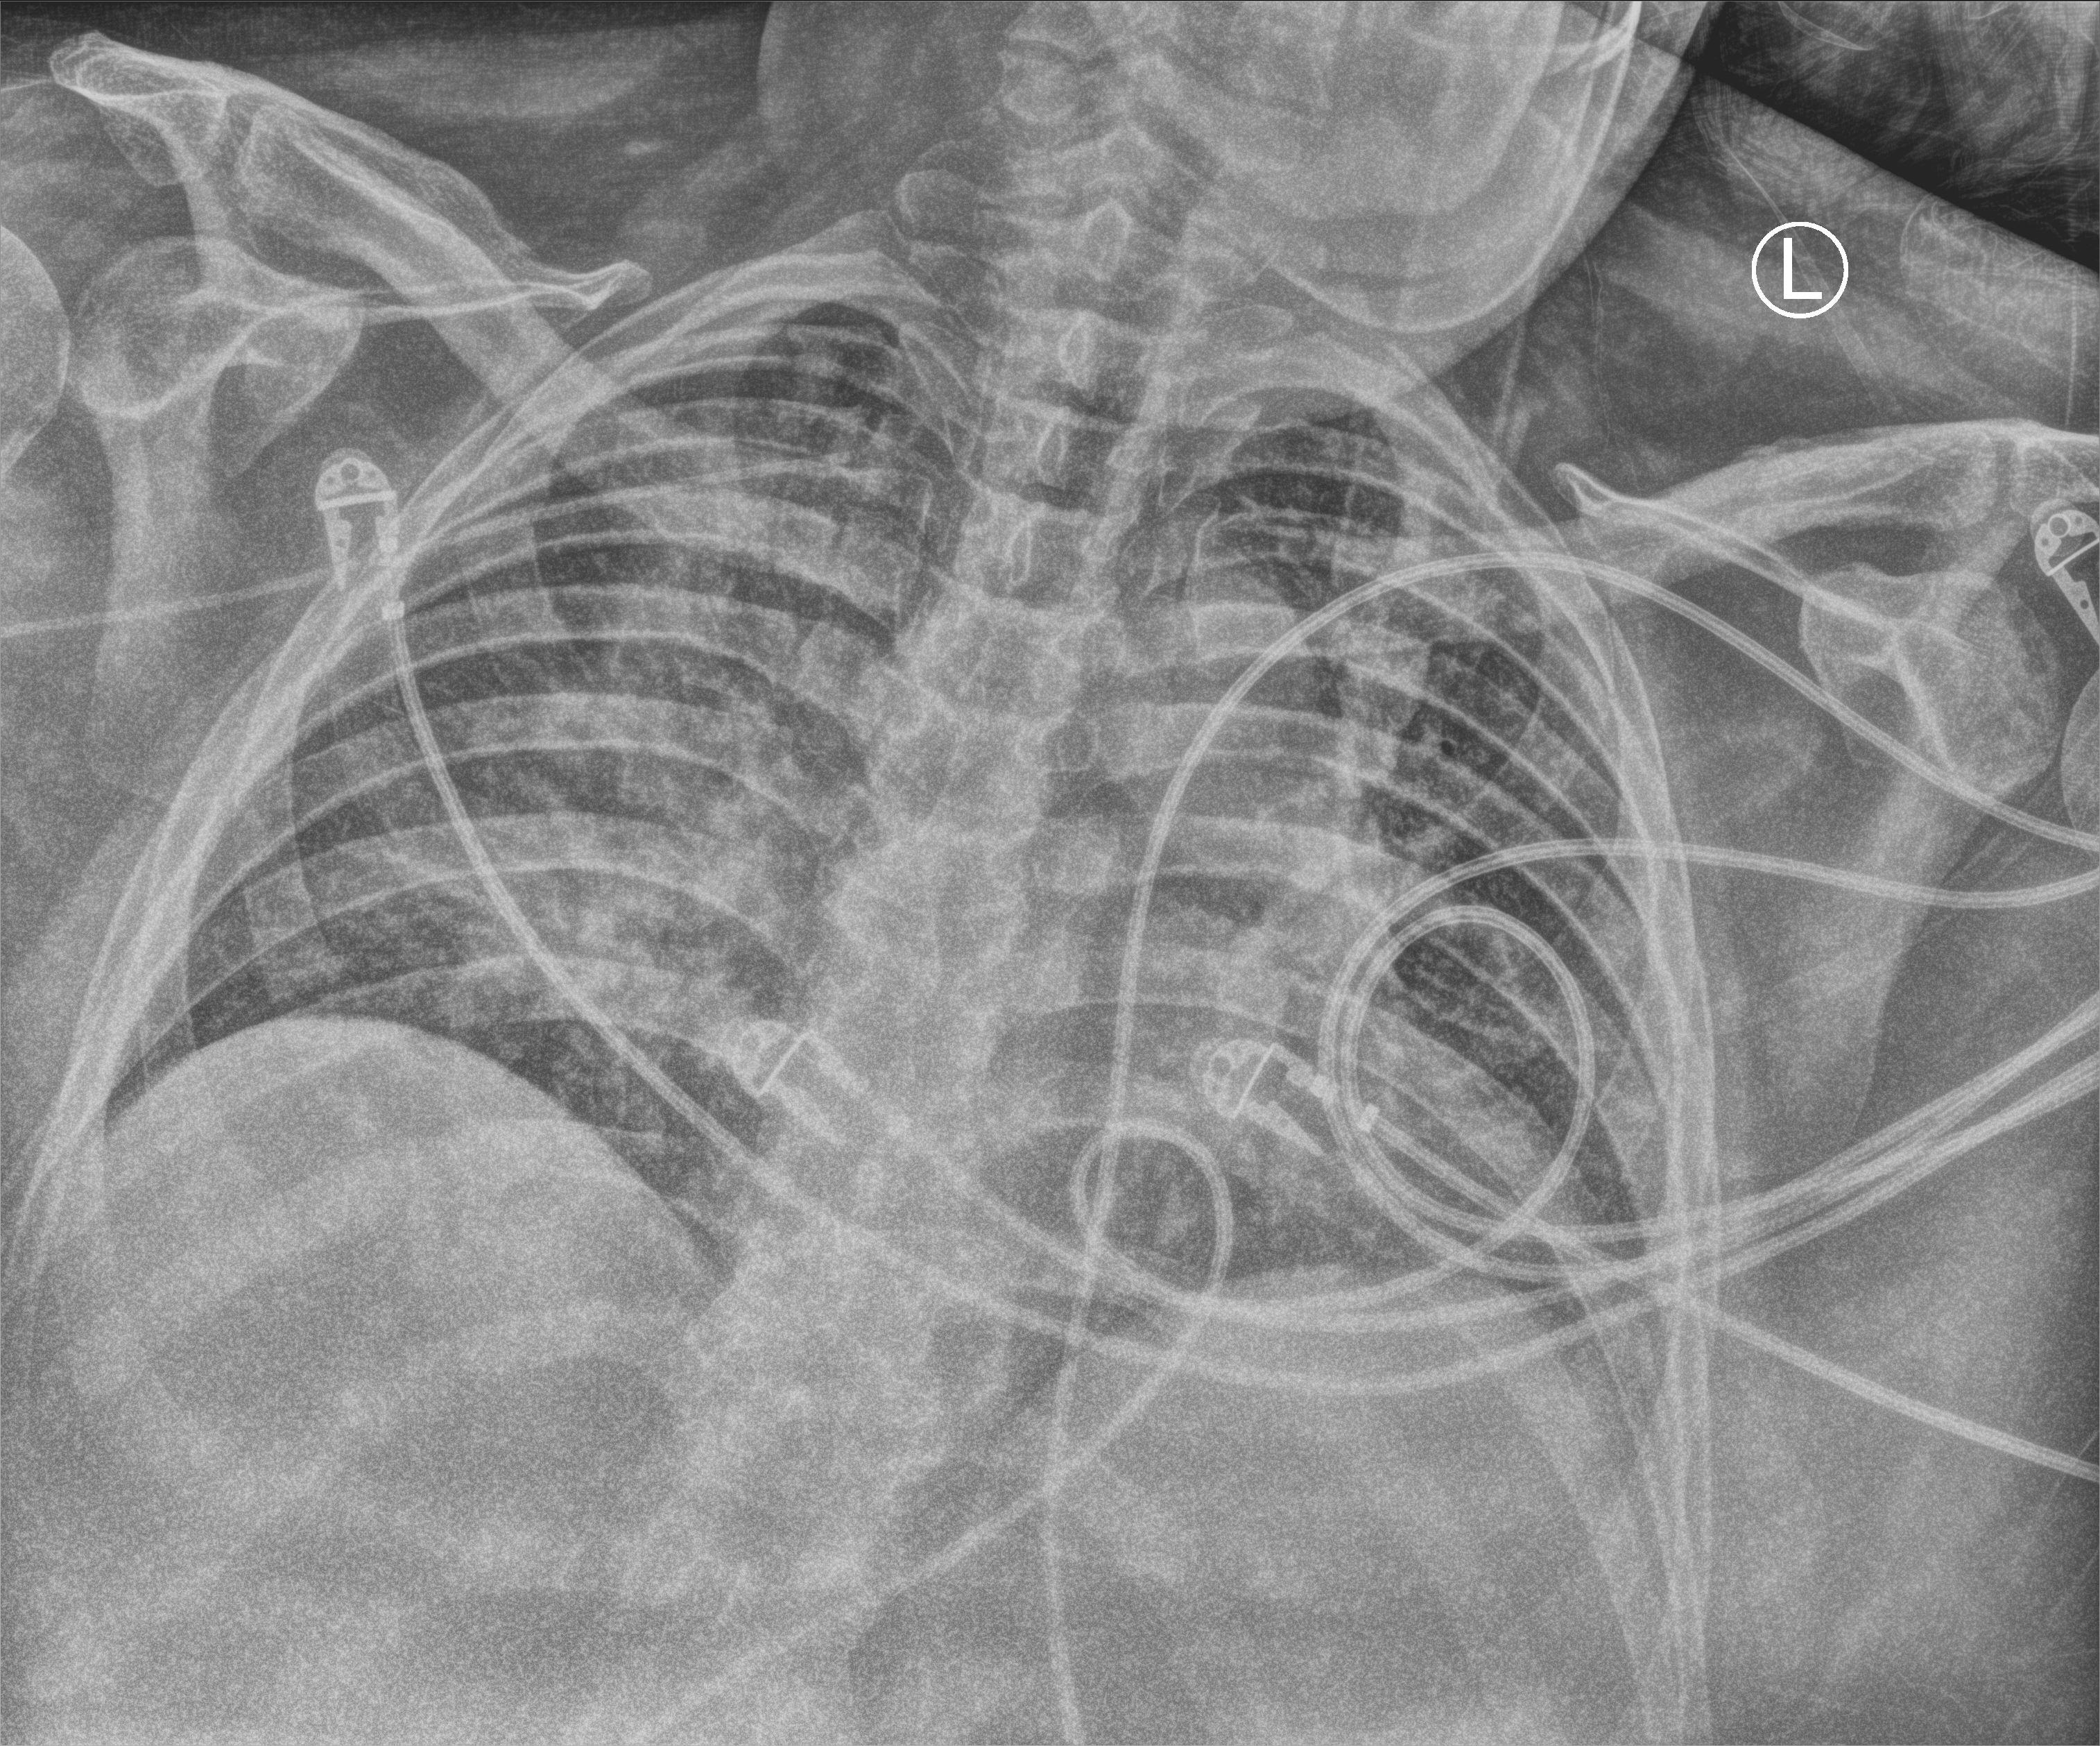
Bedside chest radiograph (computed radiography), anteroposterior (AP) projection. Patient hospitalised with COVID-19; male, aged 18–59 years.
From the hospital-stay record, not from the radiograph (when in the stay this image was taken is not recorded): admitted to intensive care during this hospital stay: yes; other chronic lung disease (admission record): no.